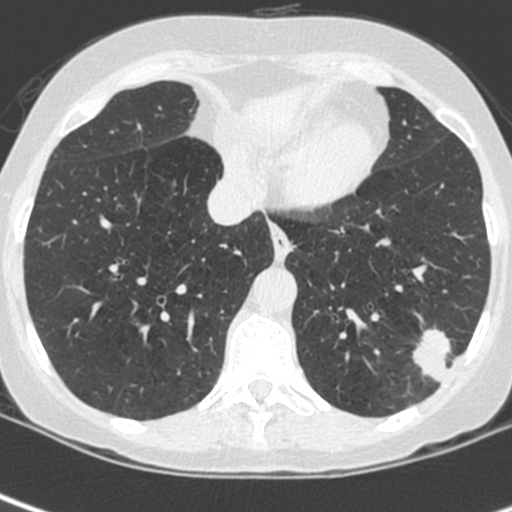
Axial slice from a low-dose chest CT screening exam; baseline annual screen; lung window (W 1500 / L -600 HU); 1.3 mm slice thickness; 120 kVp; slice 166 of 252 in the series. Female, age 56 years at enrolment. Current smoker at enrolment.
Expert-annotated lung lesion, bounding box [x1, y1, x2, y2] px = [408, 325, 473, 389]. Screening reader's record for this exam (one nodule recorded; not confirmed to be the boxed lesion): non-calcified nodule or mass ≥4 mm, left lower lobe, 37 × 29 mm, spiculated (stellate) margins, ground glass attenuation. Official screen result: positive, change unspecified: nodule(s) >= 4 mm or enlarging nodule(s), mass(es), or other non-specific abnormalities suspicious for lung cancer. Later outcome: lung cancer diagnosed 91 days after this screen — squamous cell carcinoma, NOS, left lower lobe, poorly differentiated (G3), stage IIIA (AJCC 6th edition), 35 mm at pathology.